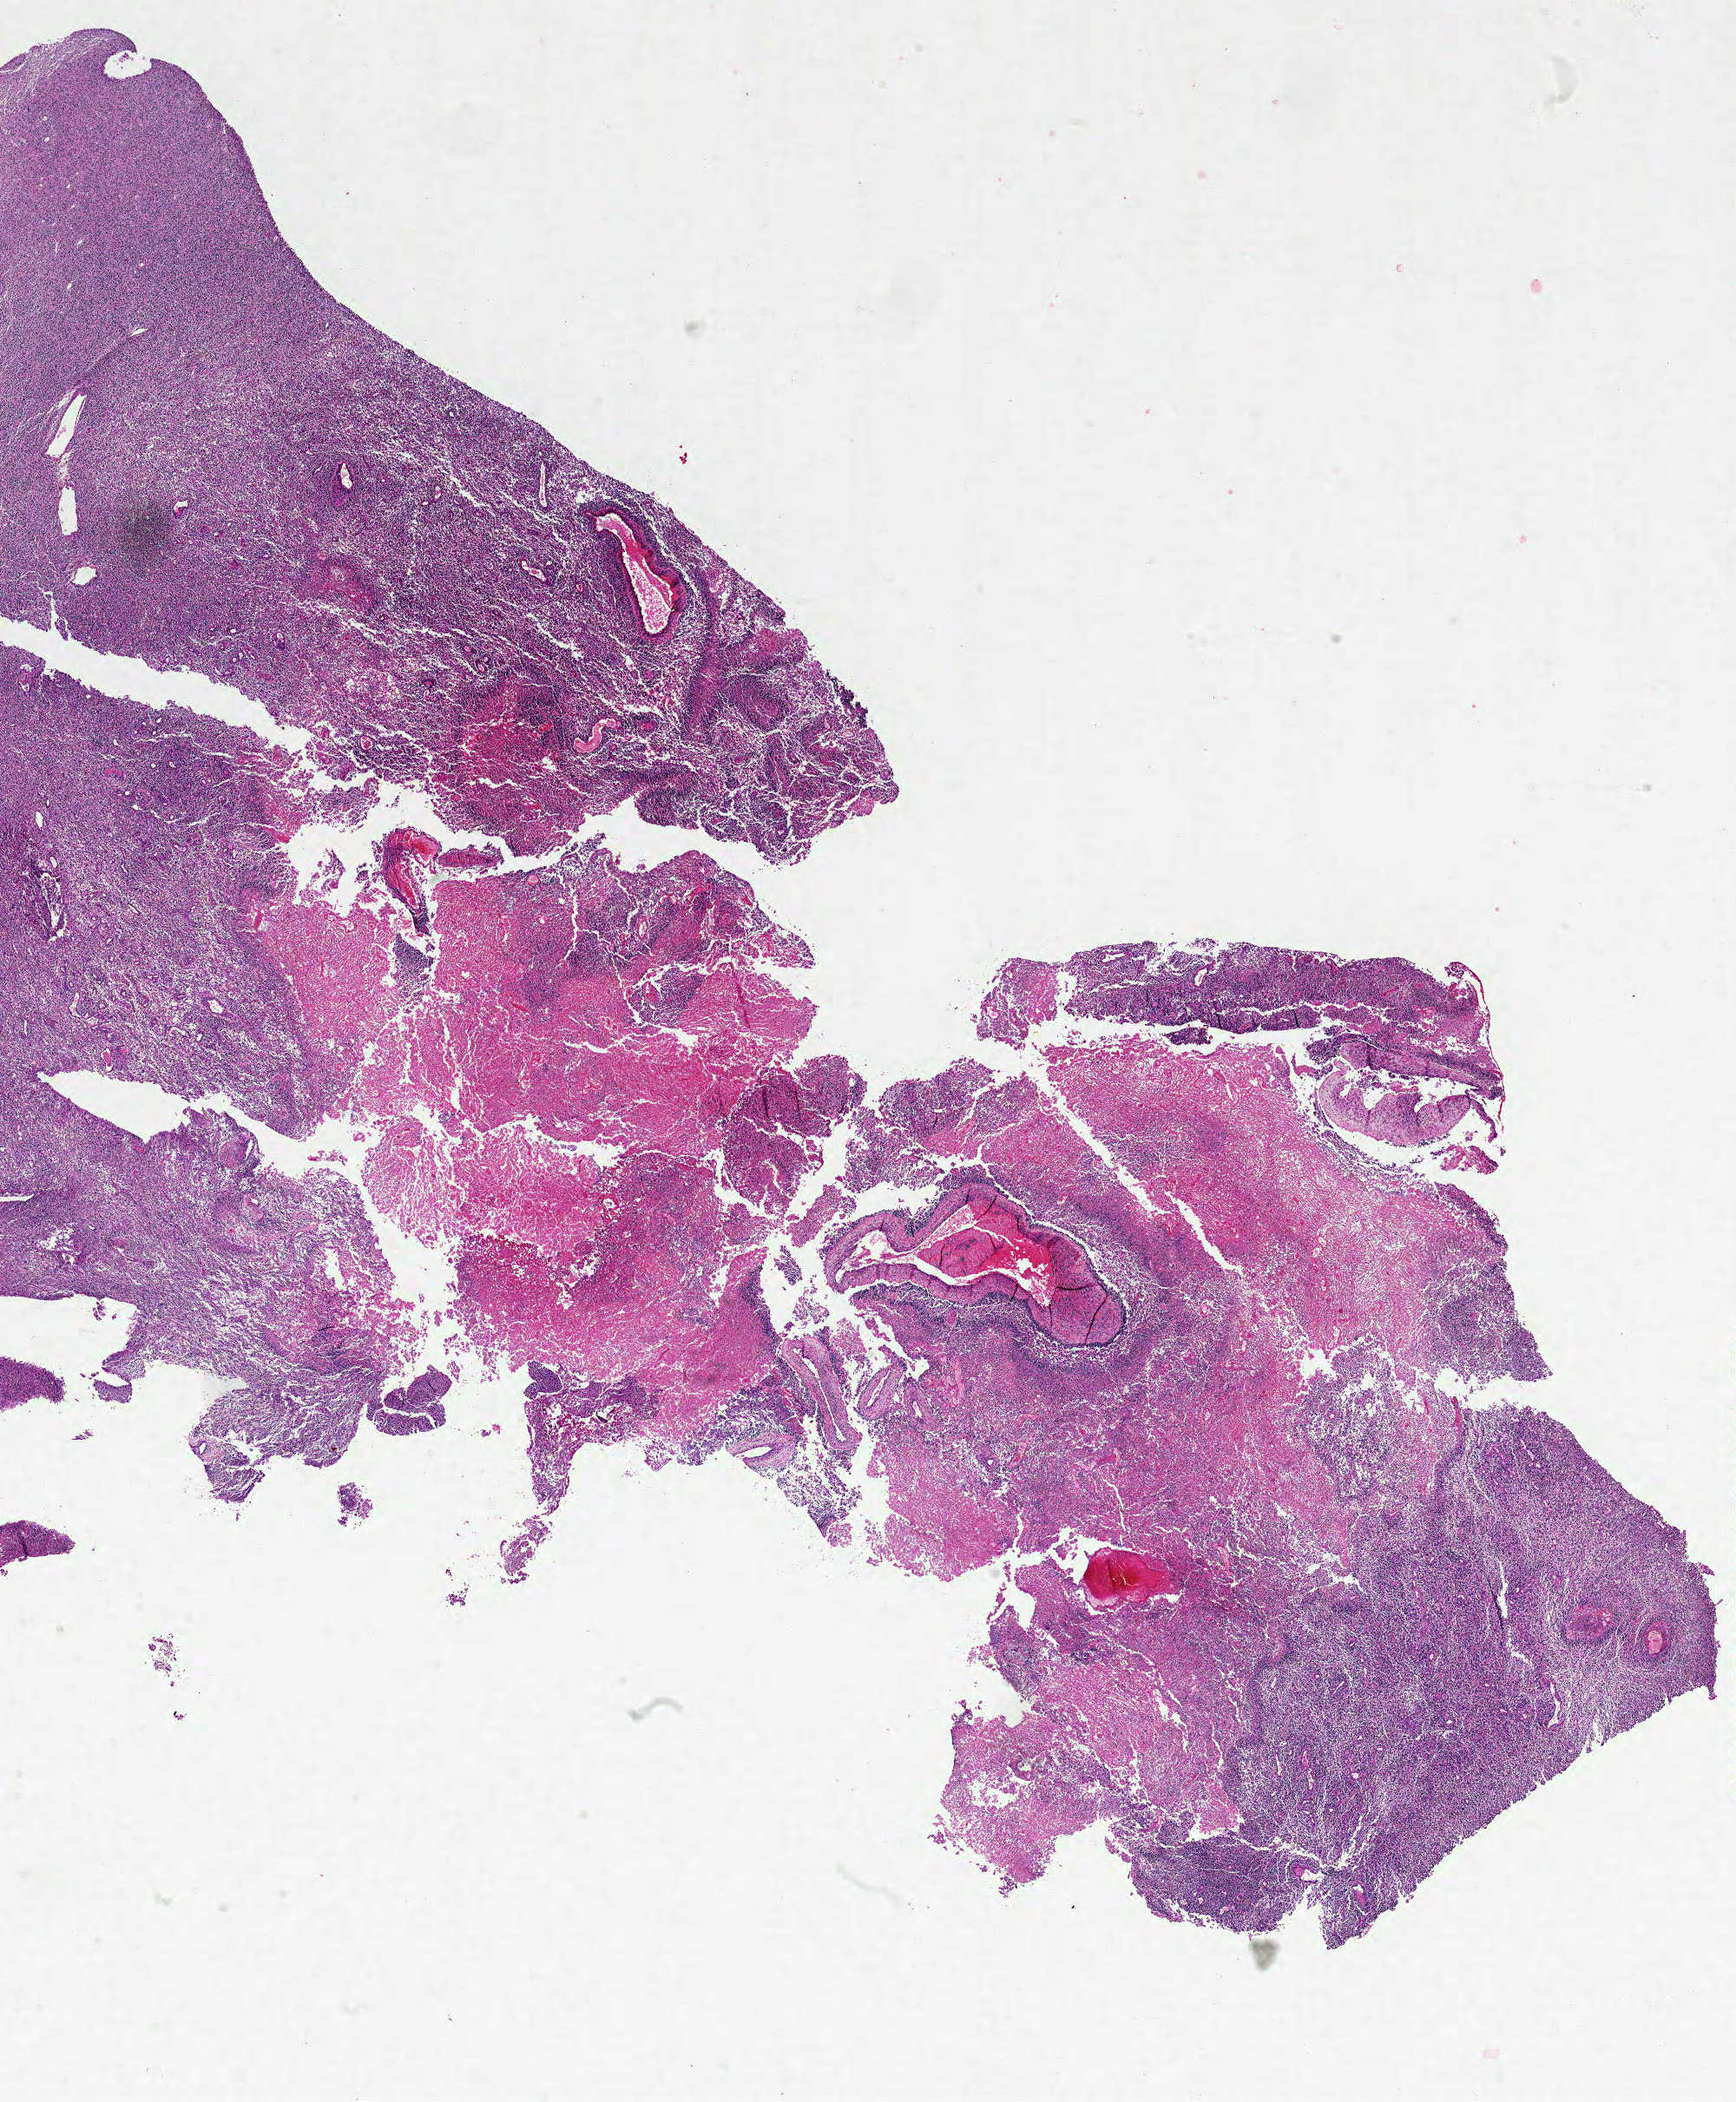
H&E-stained whole-slide image, shown as a low-resolution overview of the whole scanned area (about 16.0 x 19.4 mm, from a 20x scan), formalin-fixed paraffin-embedded (FFPE) diagnostic section, sample: primary tumour, brain. Female patient; age at initial diagnosis 51 years.
* diagnosis: Glioblastoma